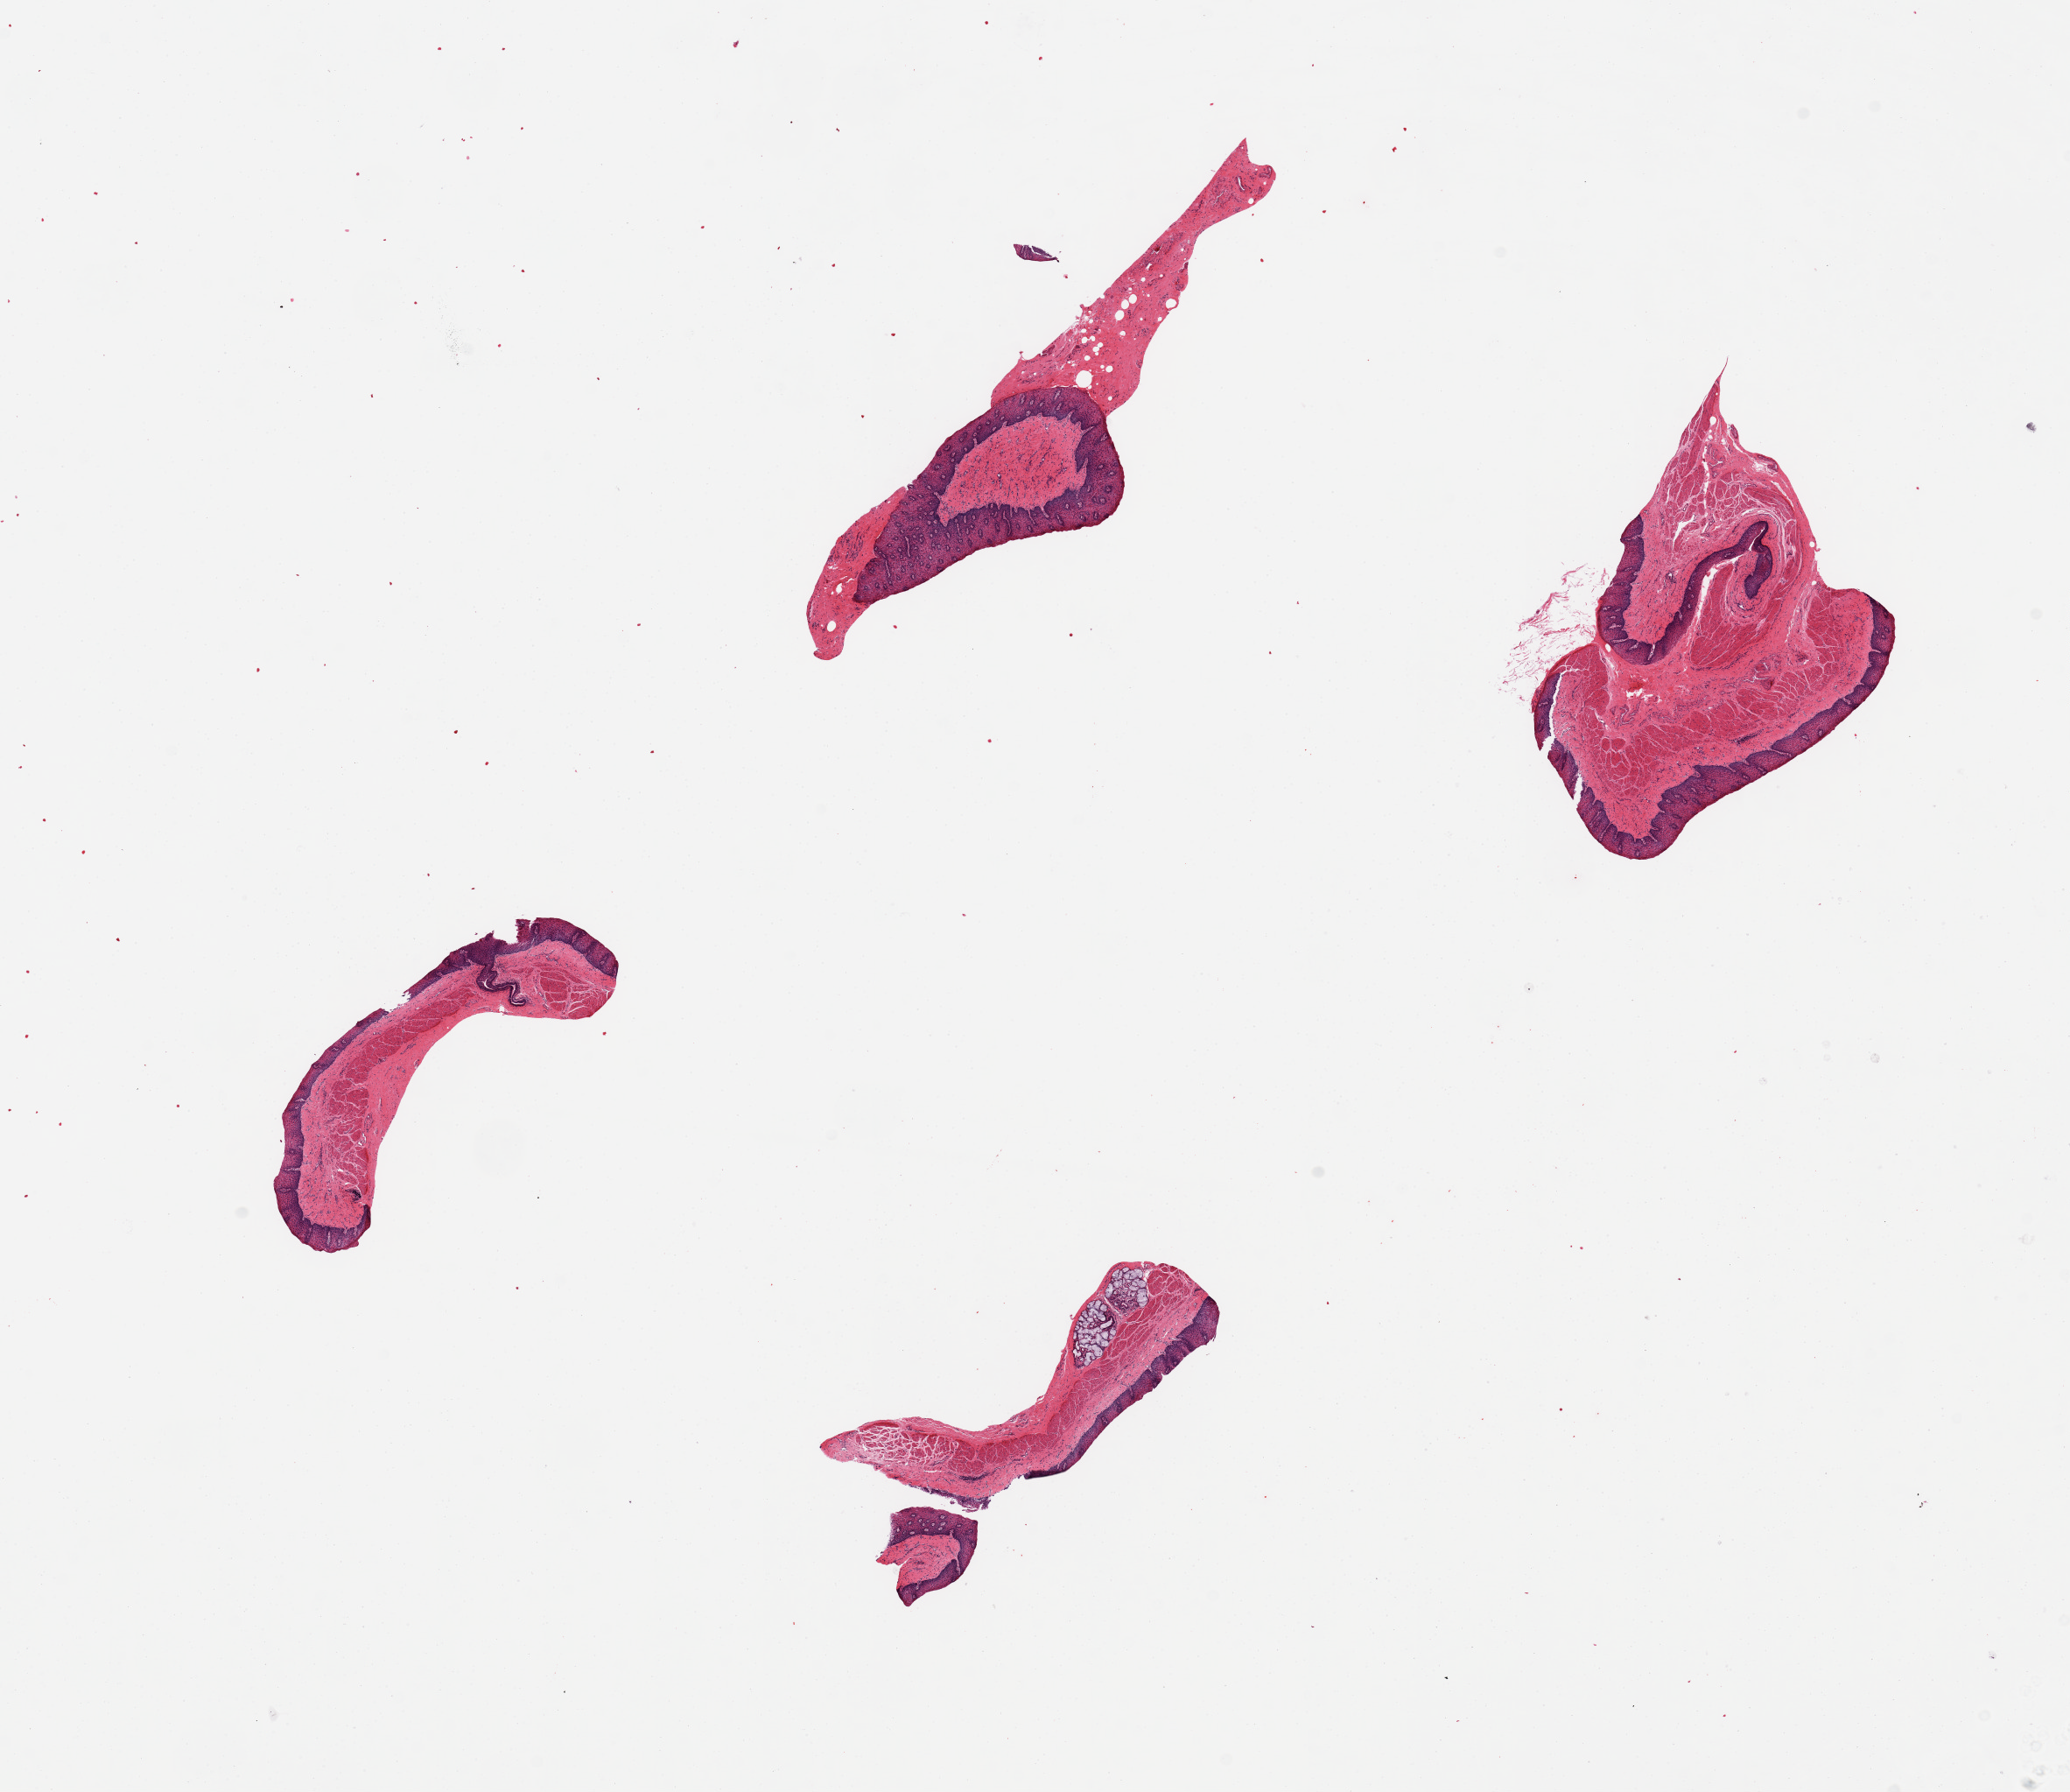
Hematoxylin and eosin (H&E) whole-slide image, brightfield, whole scanned area (about 18.7 x 16.2 mm) shown as a low-resolution overview. PAXgene-fixed, paraffin-embedded tissue. Section of esophageal mucous membrane (target tissue). Donor tissue sample. Female donor.
Pathologist's review note for this sample: 4 pieces, includes few submucosal glands.